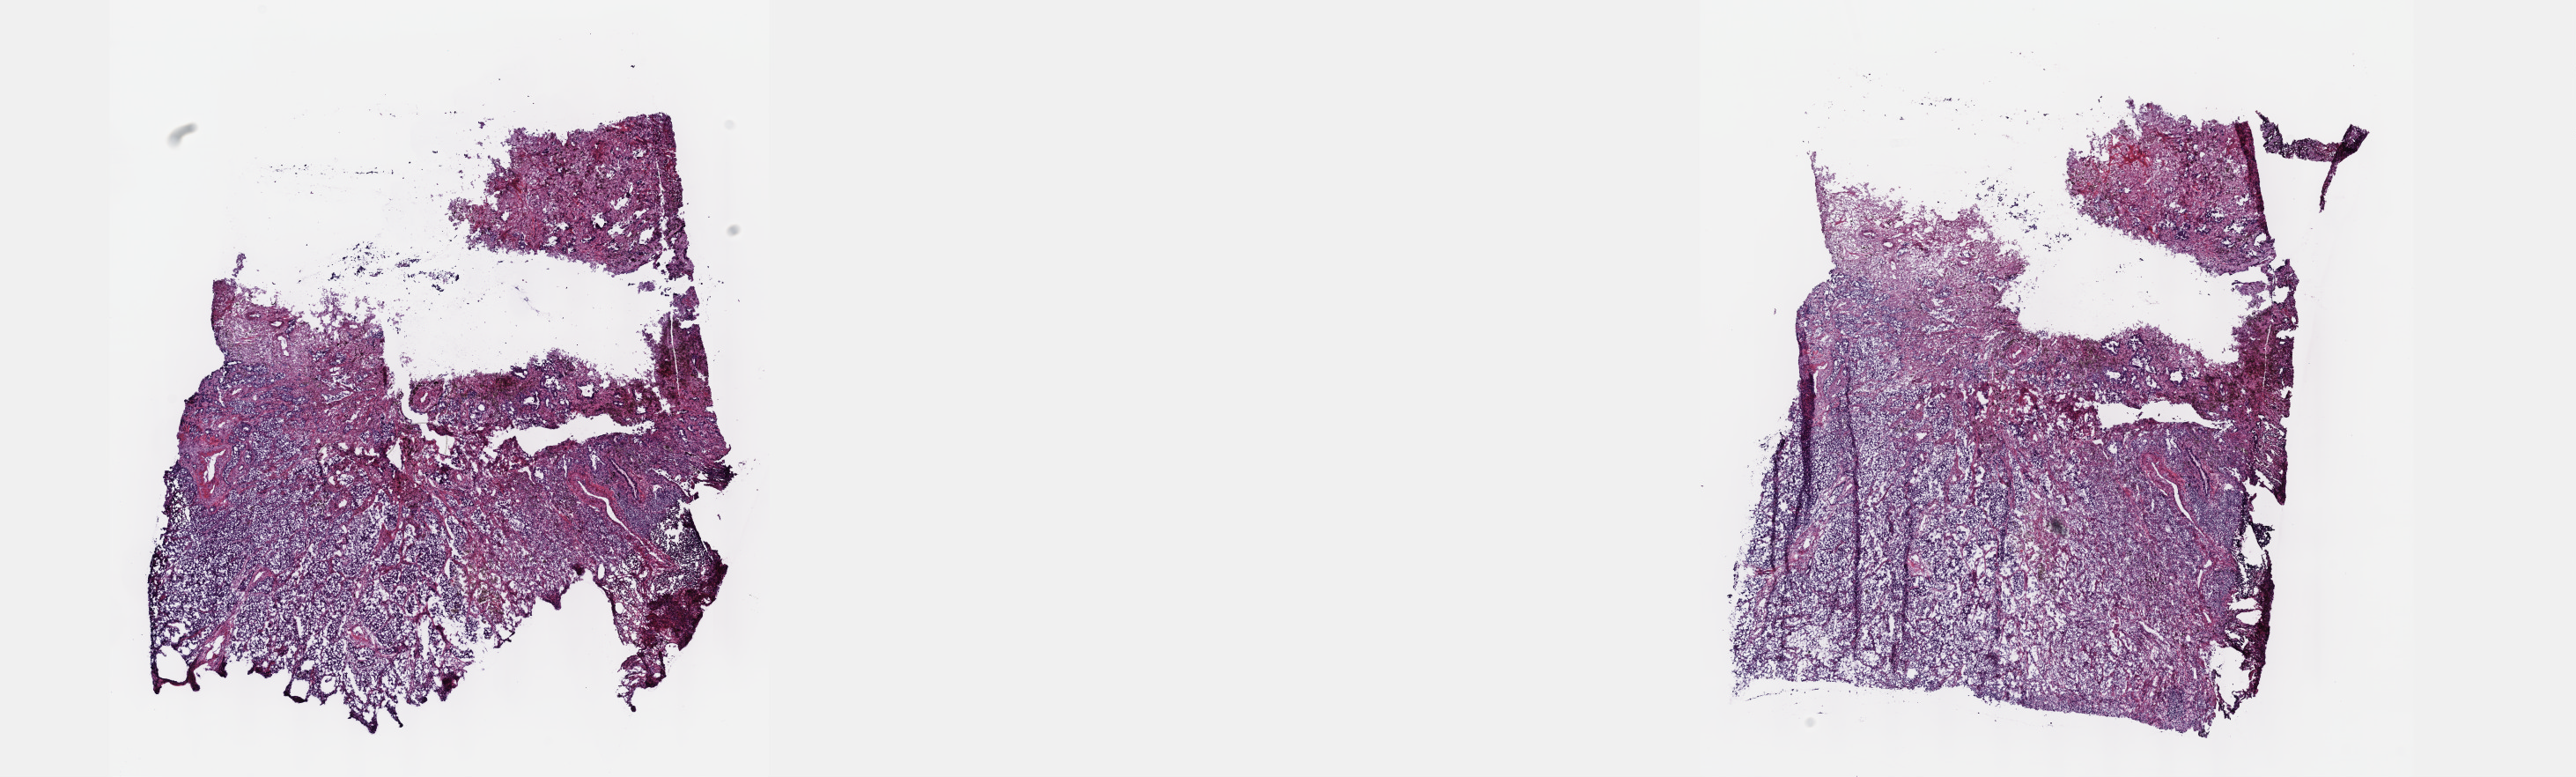
H&E-stained whole-slide image — shown as a low-resolution overview of the whole scanned area (about 23.6 x 7.1 mm, slide scanned at 40x), frozen section, lung, primary tumour sample. Patient: male, age at initial diagnosis 57 years. Composition of this section per pathologist review: tumour cells 100%, tumour nuclei 70%, normal cells 0%, stromal cells 0%, necrosis 0%. Inflammatory infiltration, as recorded: lymphocyte infiltration 4%, monocyte infiltration 1%, neutrophil infiltration 0%.
• histologic diagnosis: Adenocarcinoma, NOS (upper lobe, lung)
• AJCC pathologic stage: IA (5th edition)
• laterality: right